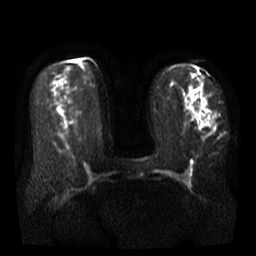
Breast MRI, one axial slice. Slice 23 of 41 in the series (ordered by position). Diffusion-weighted series; image 2 of 4 stored at this slice position (different b-values; order by instance number). 3 T. 5 mm slice thickness. 256 × 256 image matrix, field of view 340 × 340 mm. Female patient.
Annotated regions visible in this slice (expert manual segmentation):
- tumour on diffusion-weighted imaging: bounding box <196,100,209,128> (left, top, right, bottom; pixels)